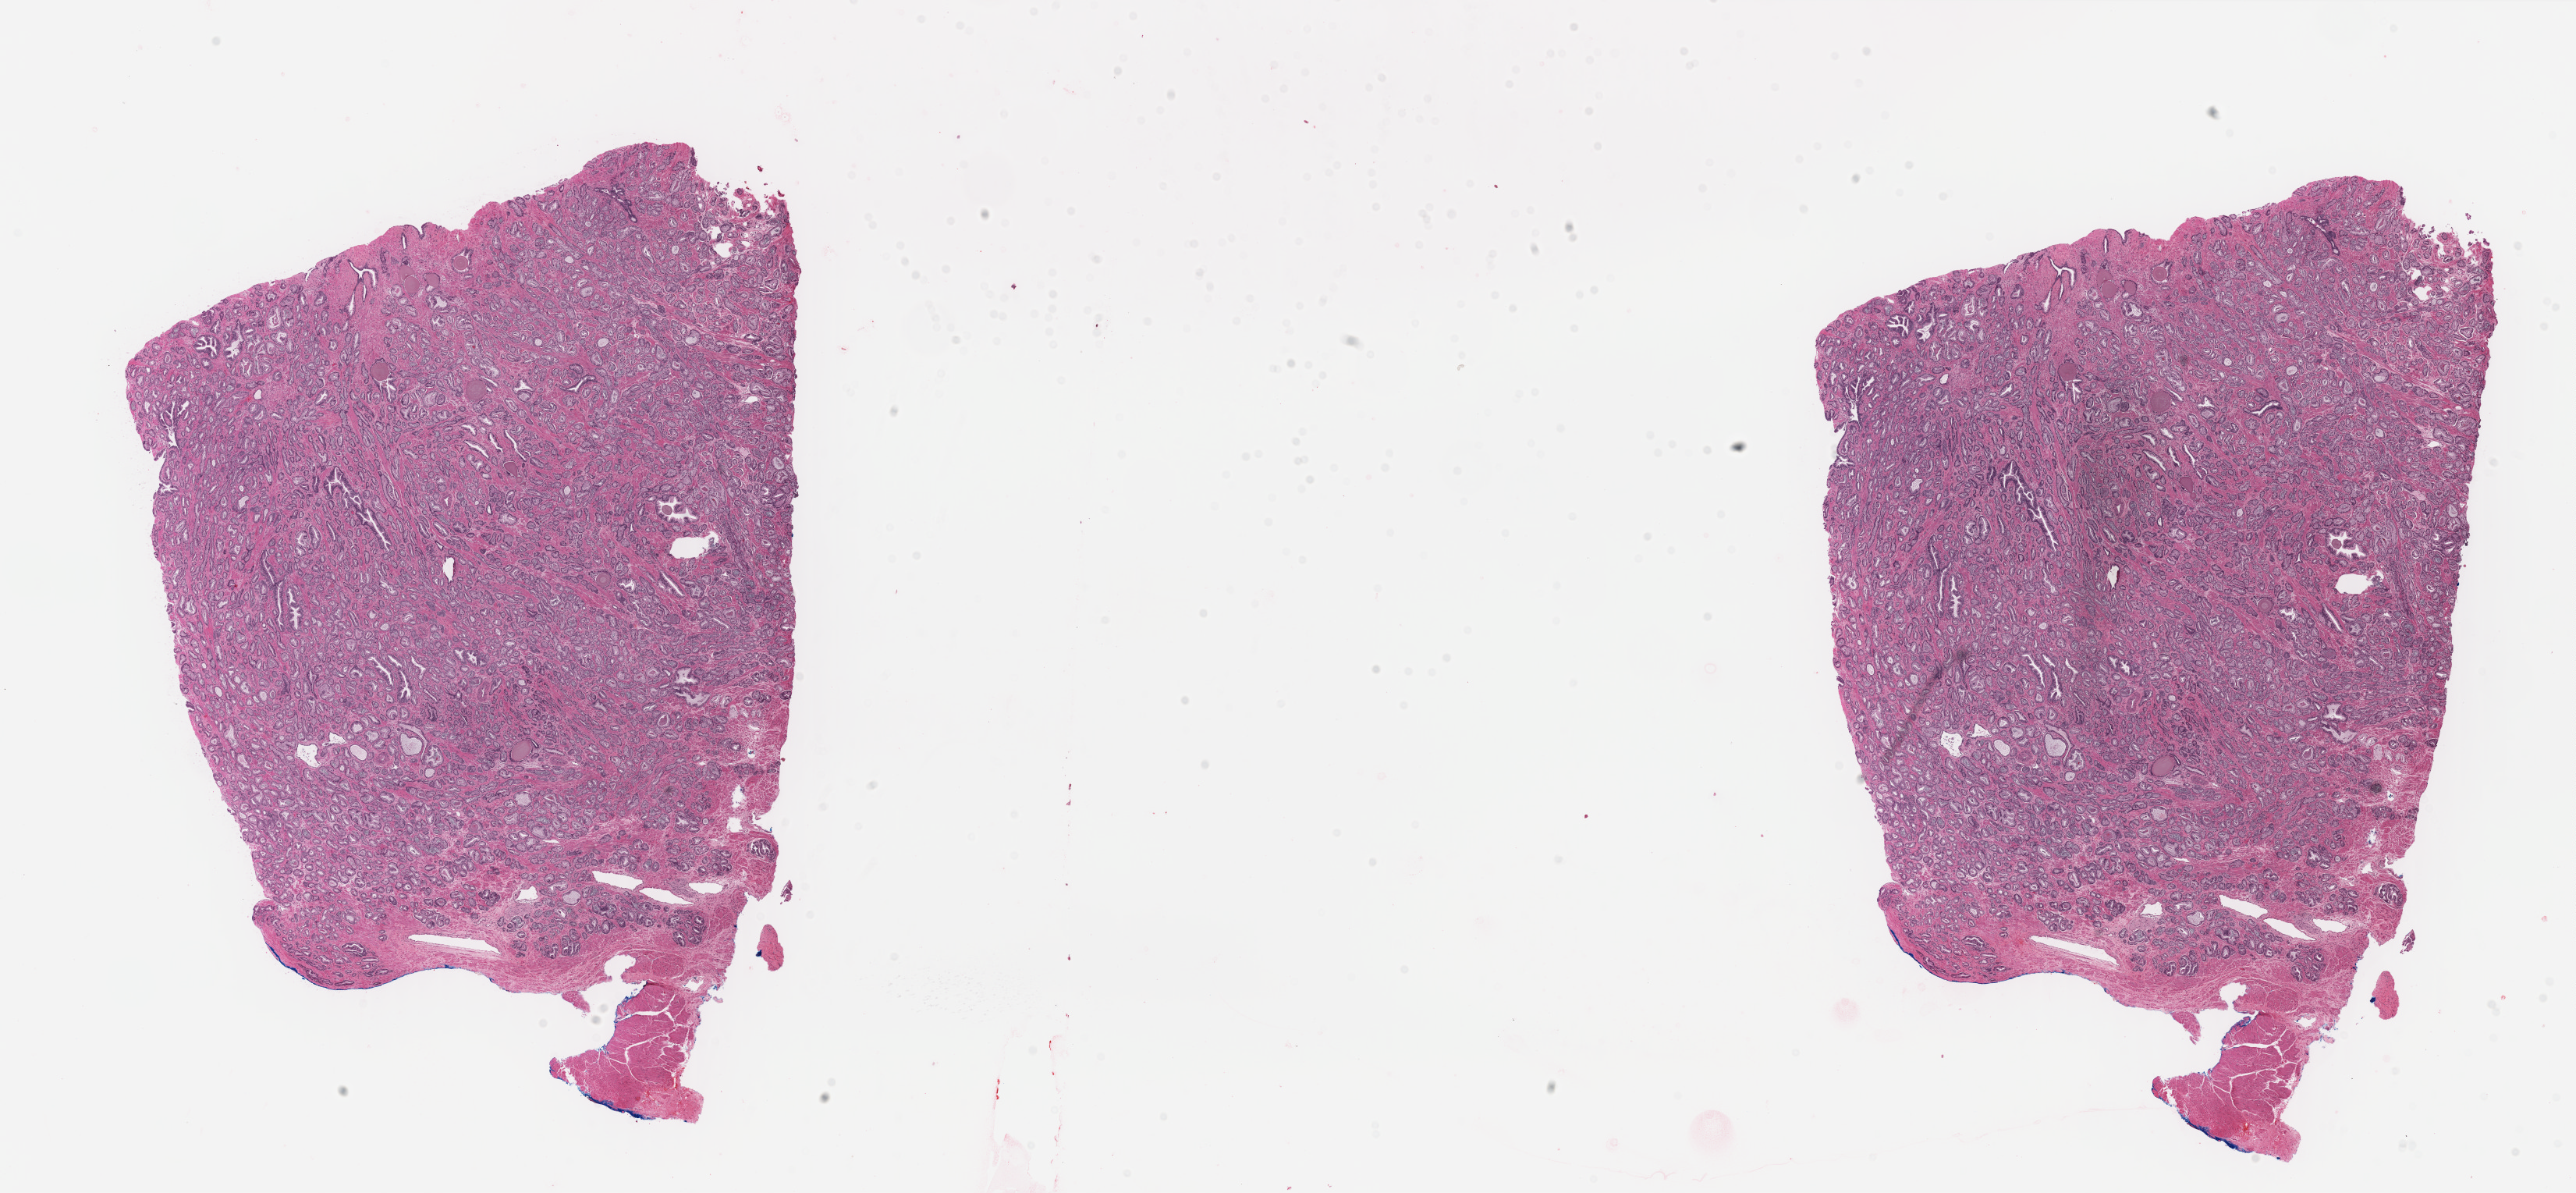
Whole-slide histology image, H&E-stained — a low-resolution overview of the entire scanned area, about 26.1 x 12.1 mm, formalin-fixed paraffin-embedded (FFPE) diagnostic section, sample: primary tumour, prostate. Male patient; age at initial diagnosis 53 years. Gleason score: 6 (3+3).
Laterality: bilateral. Pathologic diagnosis: Adenocarcinoma, NOS (prostate gland).